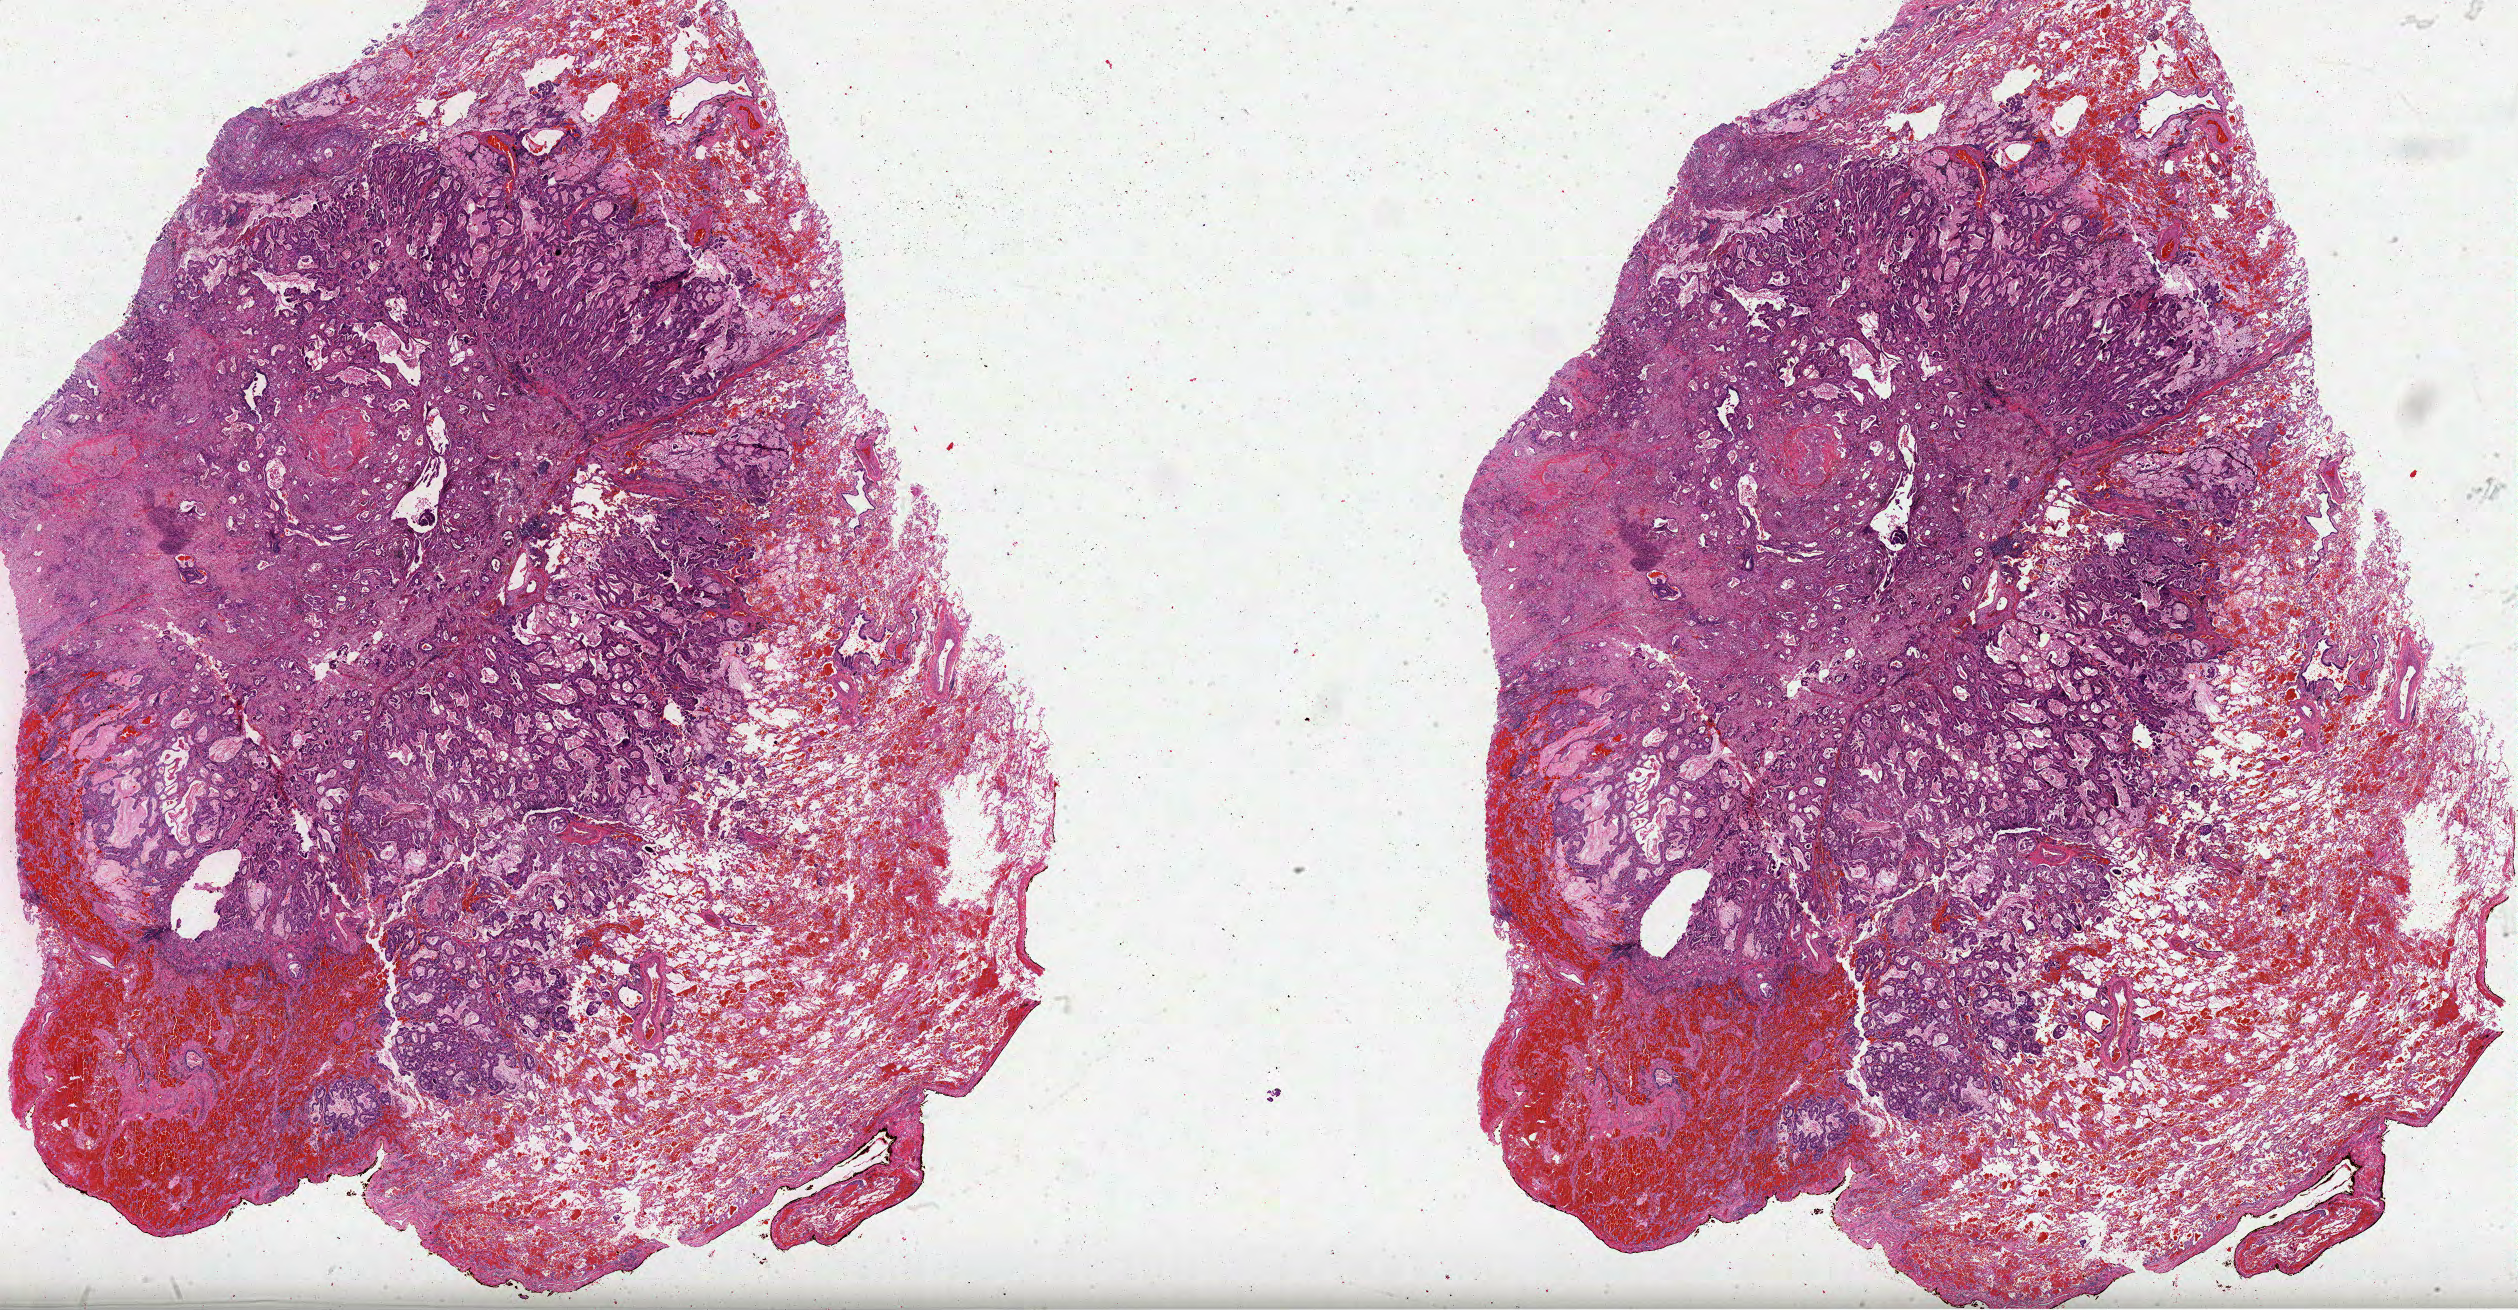
Digitized H&E-stained tissue section (whole slide) — low-resolution overview of the scanned area, about 40.6 x 21.1 mm; formalin-fixed paraffin-embedded (FFPE) diagnostic section; lung, primary tumour sample. Patient: male, age at initial diagnosis 70 years.
AJCC pathologic stage: IIA (7th edition). TNM: T2a N1 M0. Histologic diagnosis: Mucinous adenocarcinoma (upper lobe, lung). Laterality: left.